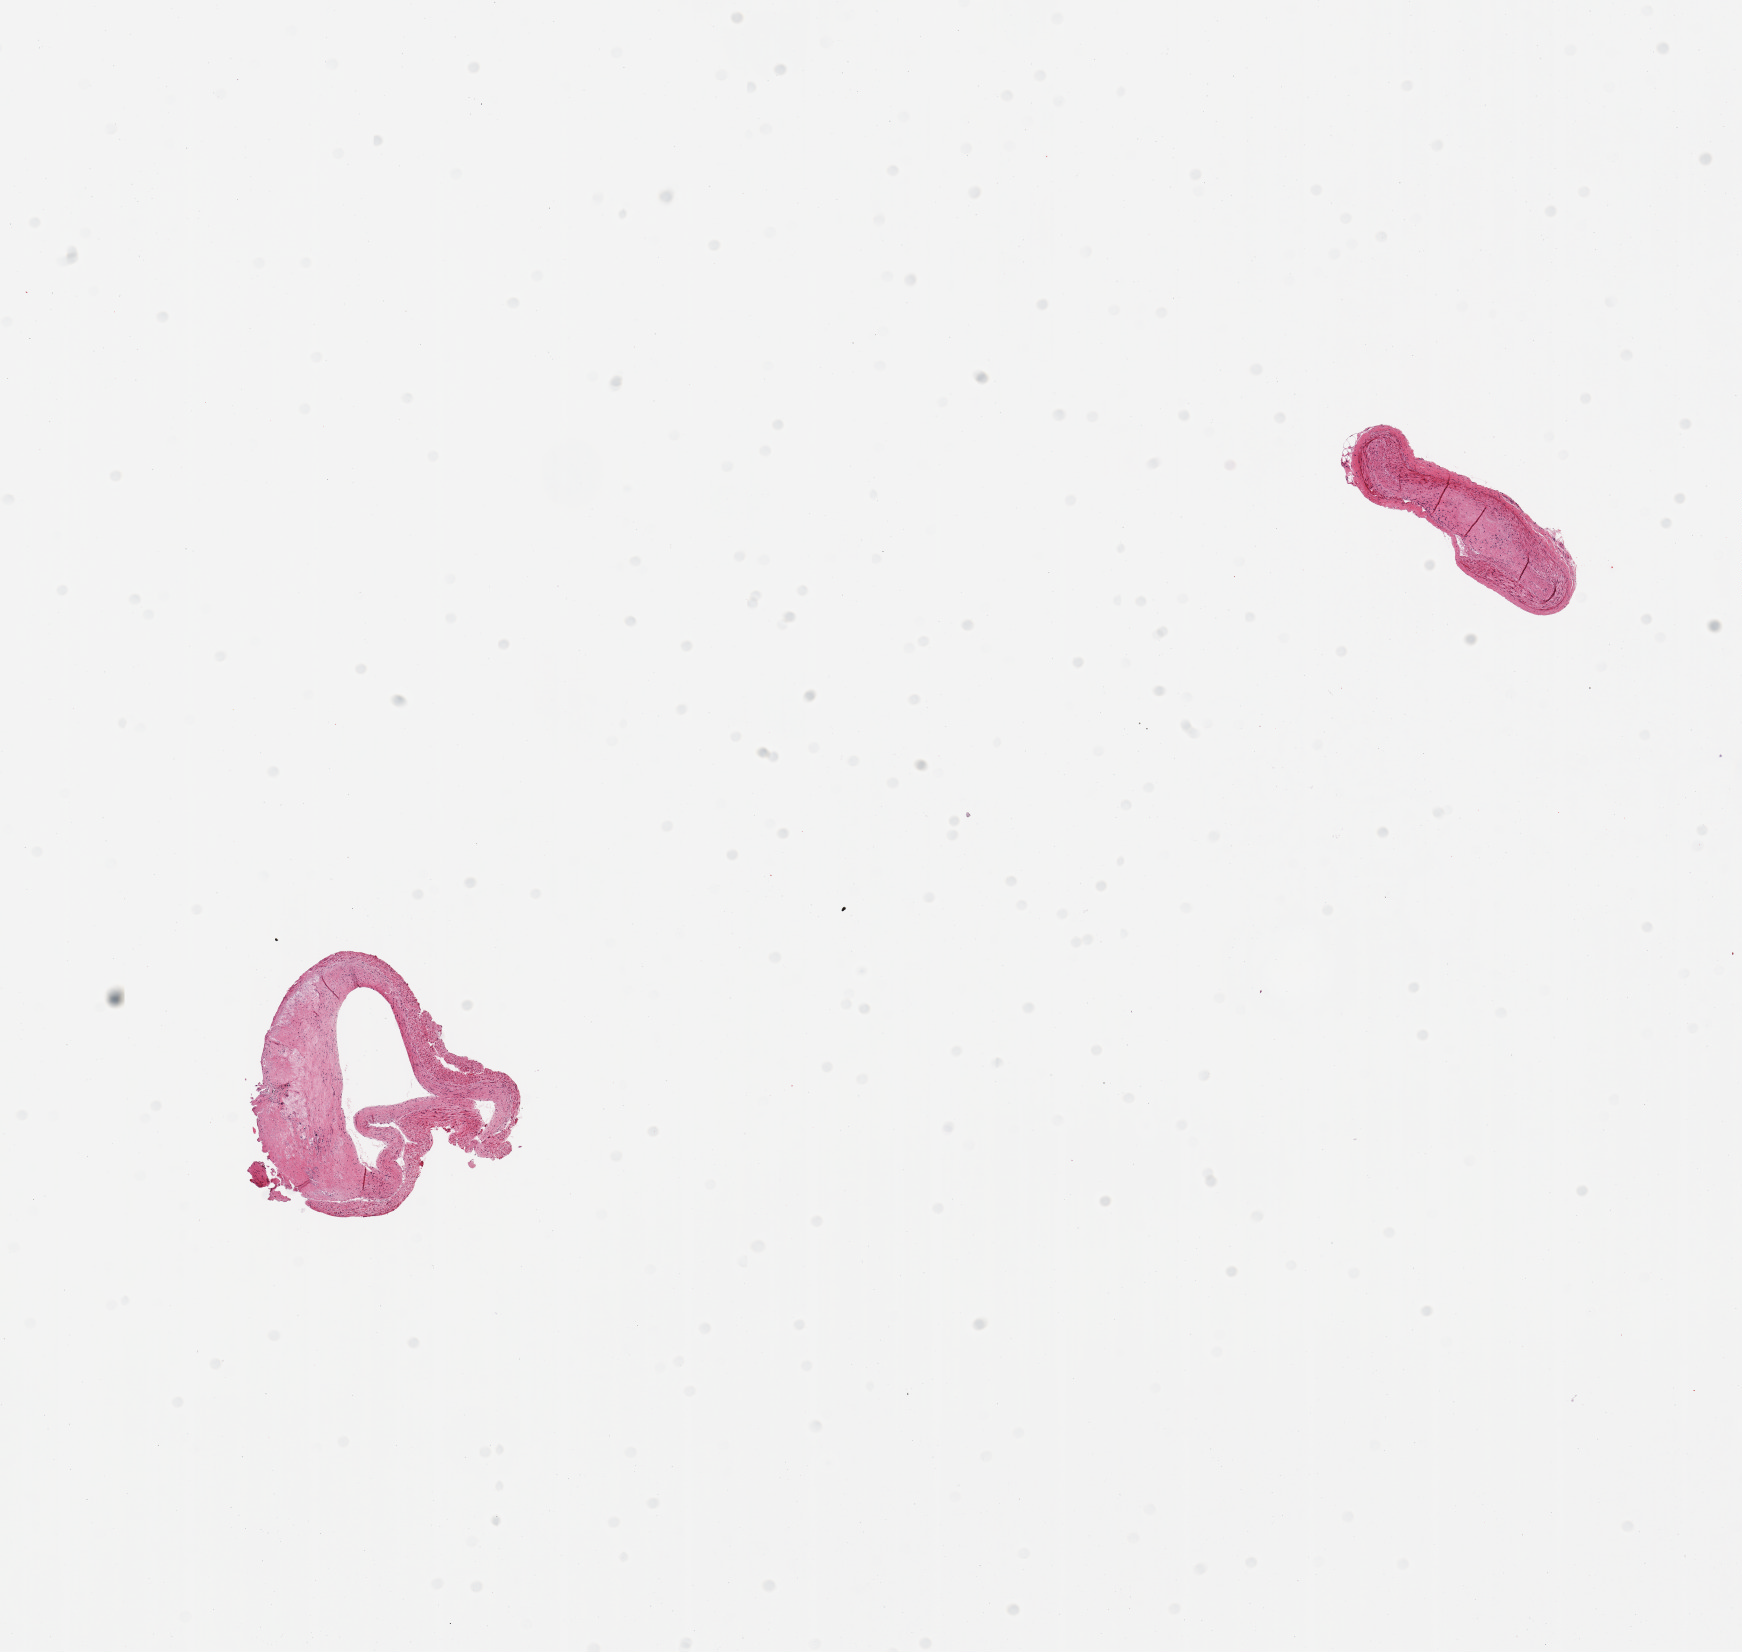
Digitized hematoxylin and eosin (H&E)-stained section, brightfield — low-resolution overview of the scanned area, about 13.8 x 13.1 mm (from a 20x scan). PAXgene-fixed paraffin-embedded (PFPE) section. Section of coronary artery (target tissue). Tissue donor sample. Male donor.
- pathologist's review note for this sample: 2 pieces; atherosclerosis